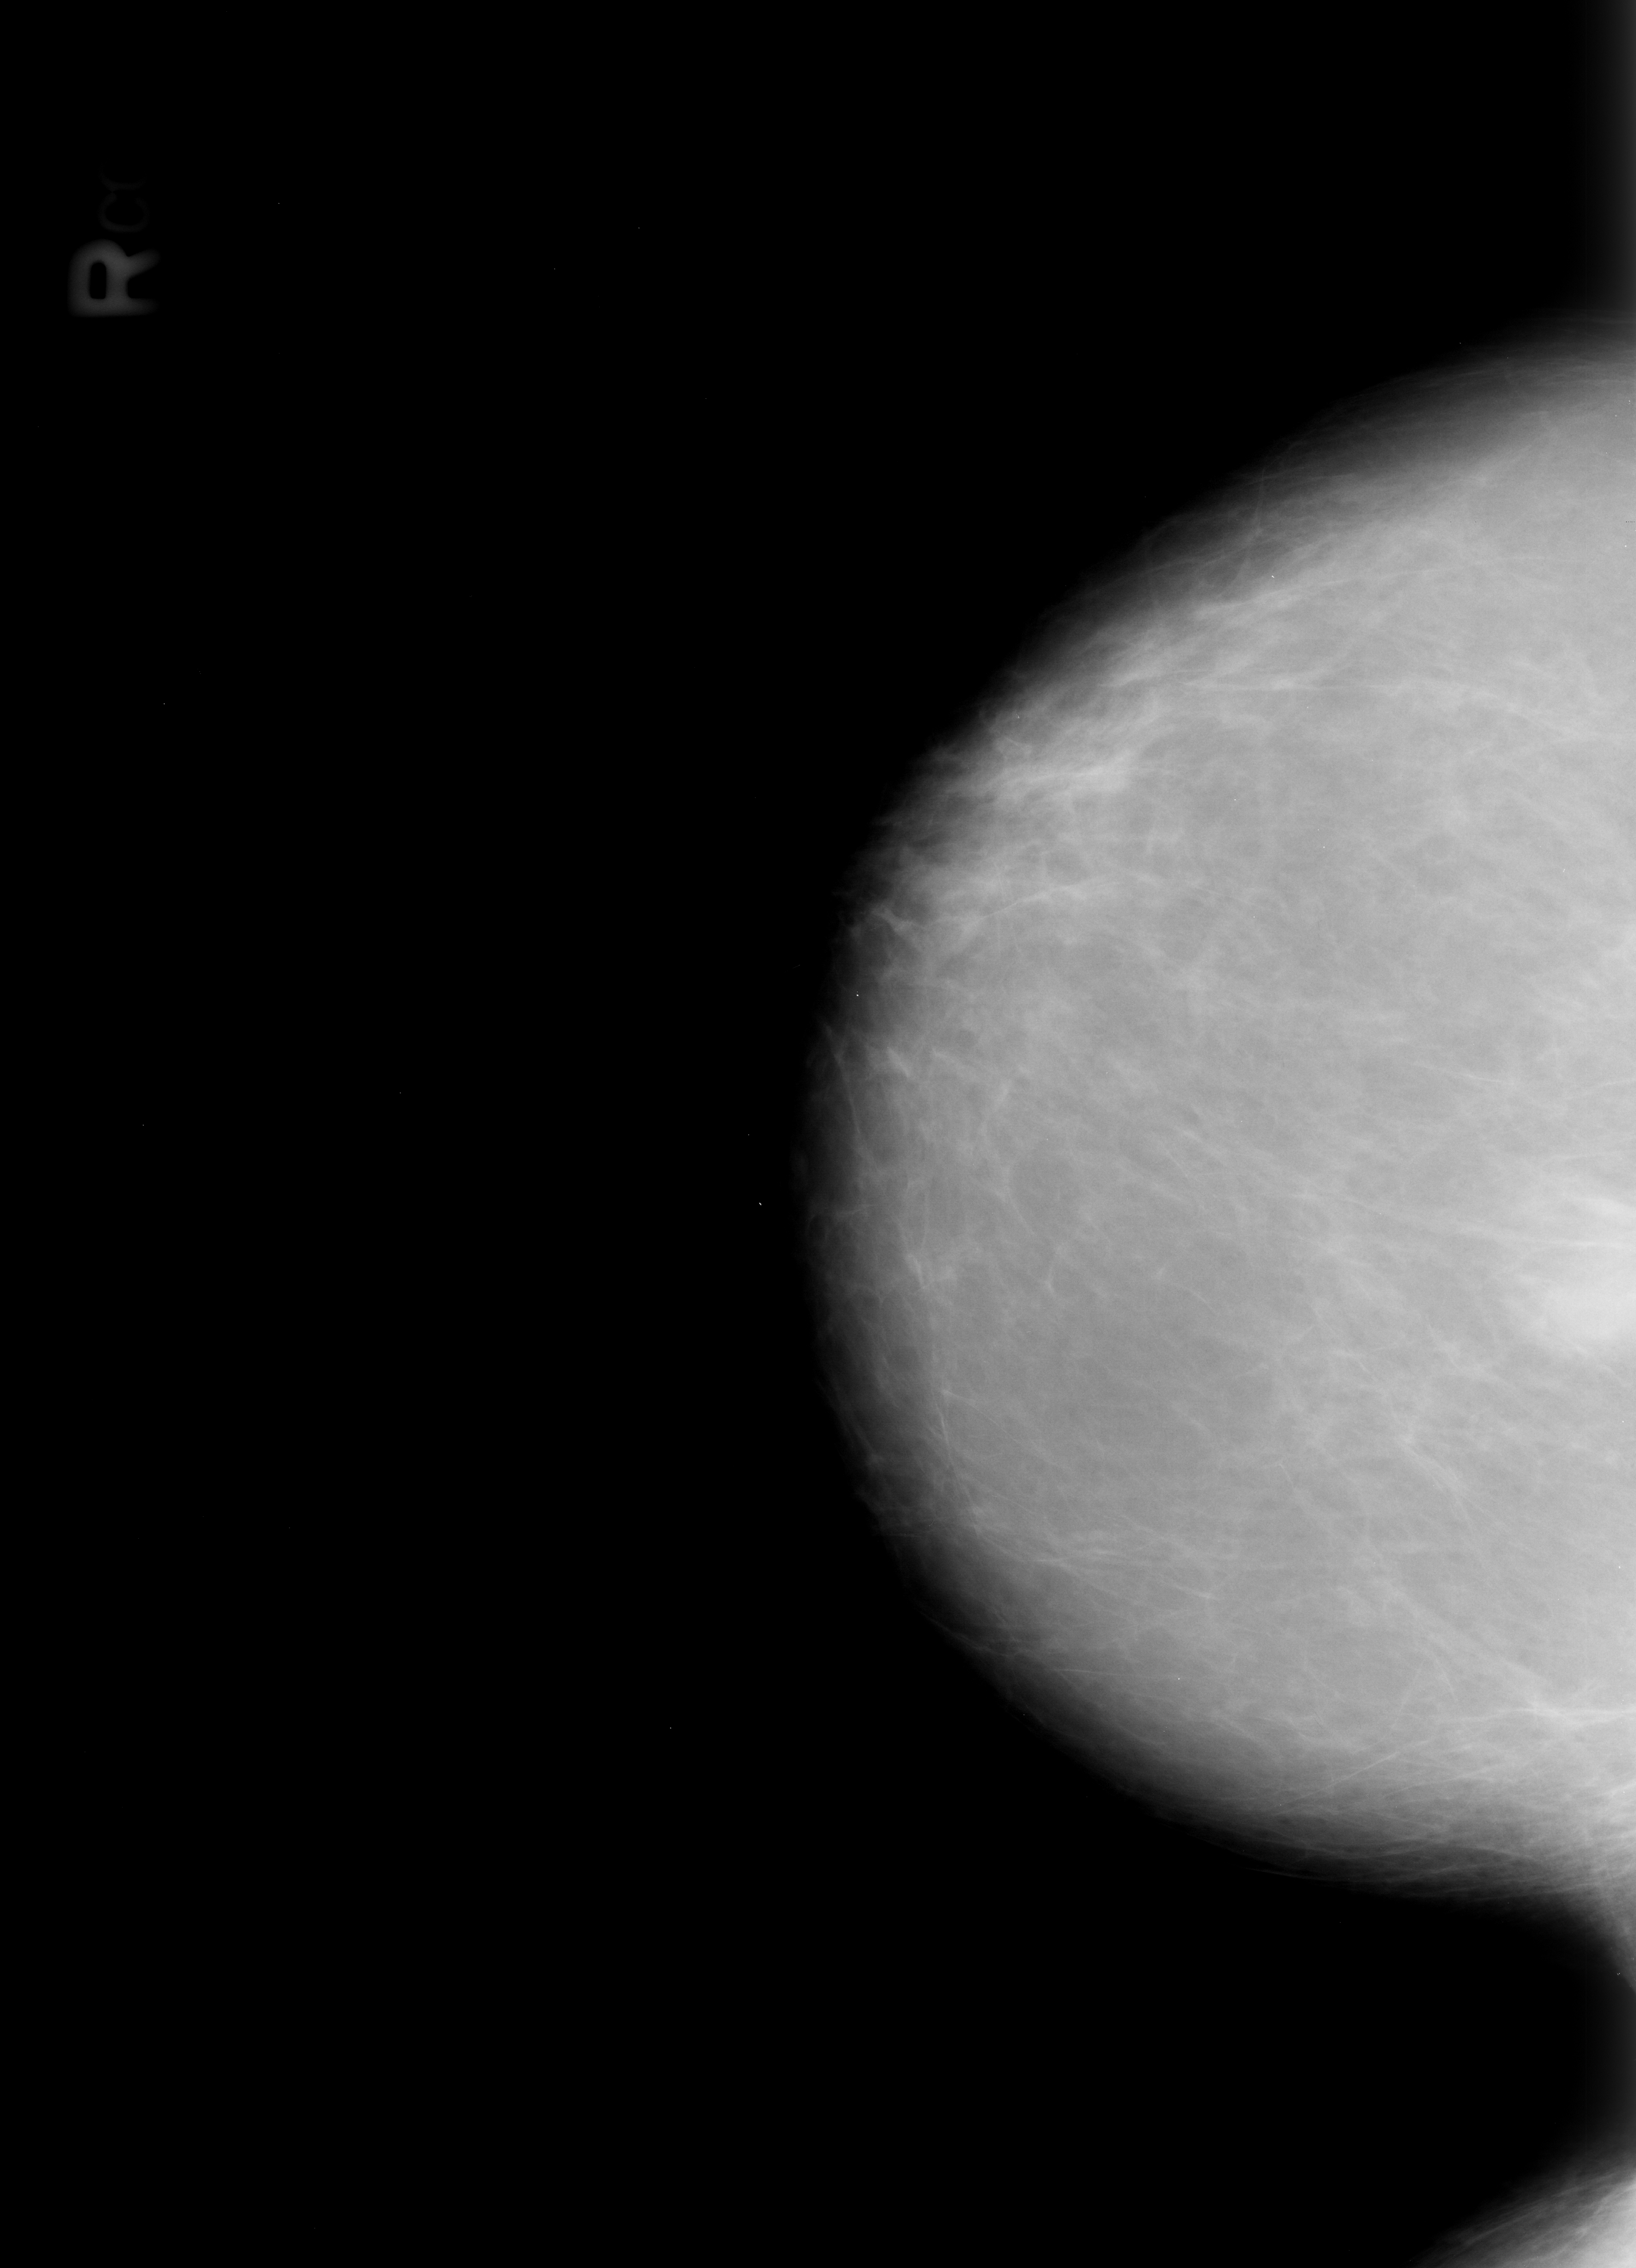
Scanned film-screen mammogram; right breast; CC view; breast composition: scattered fibroglandular densities (BI-RADS density category 2 of 4); 1636 × 2268 image matrix.
Marked abnormalities (boxes around the expert regions of interest):
- mass, shape asymmetric breast tissue; BI-RADS assessment category 2; subtlety rating 4 on a 1 (subtle) to 5 (obvious) scale; benign; no additional work-up was recommended (outcome (as recorded, no biopsy): benign without callback): box from (x=1537, y=1254) to (x=1636, y=1373) px